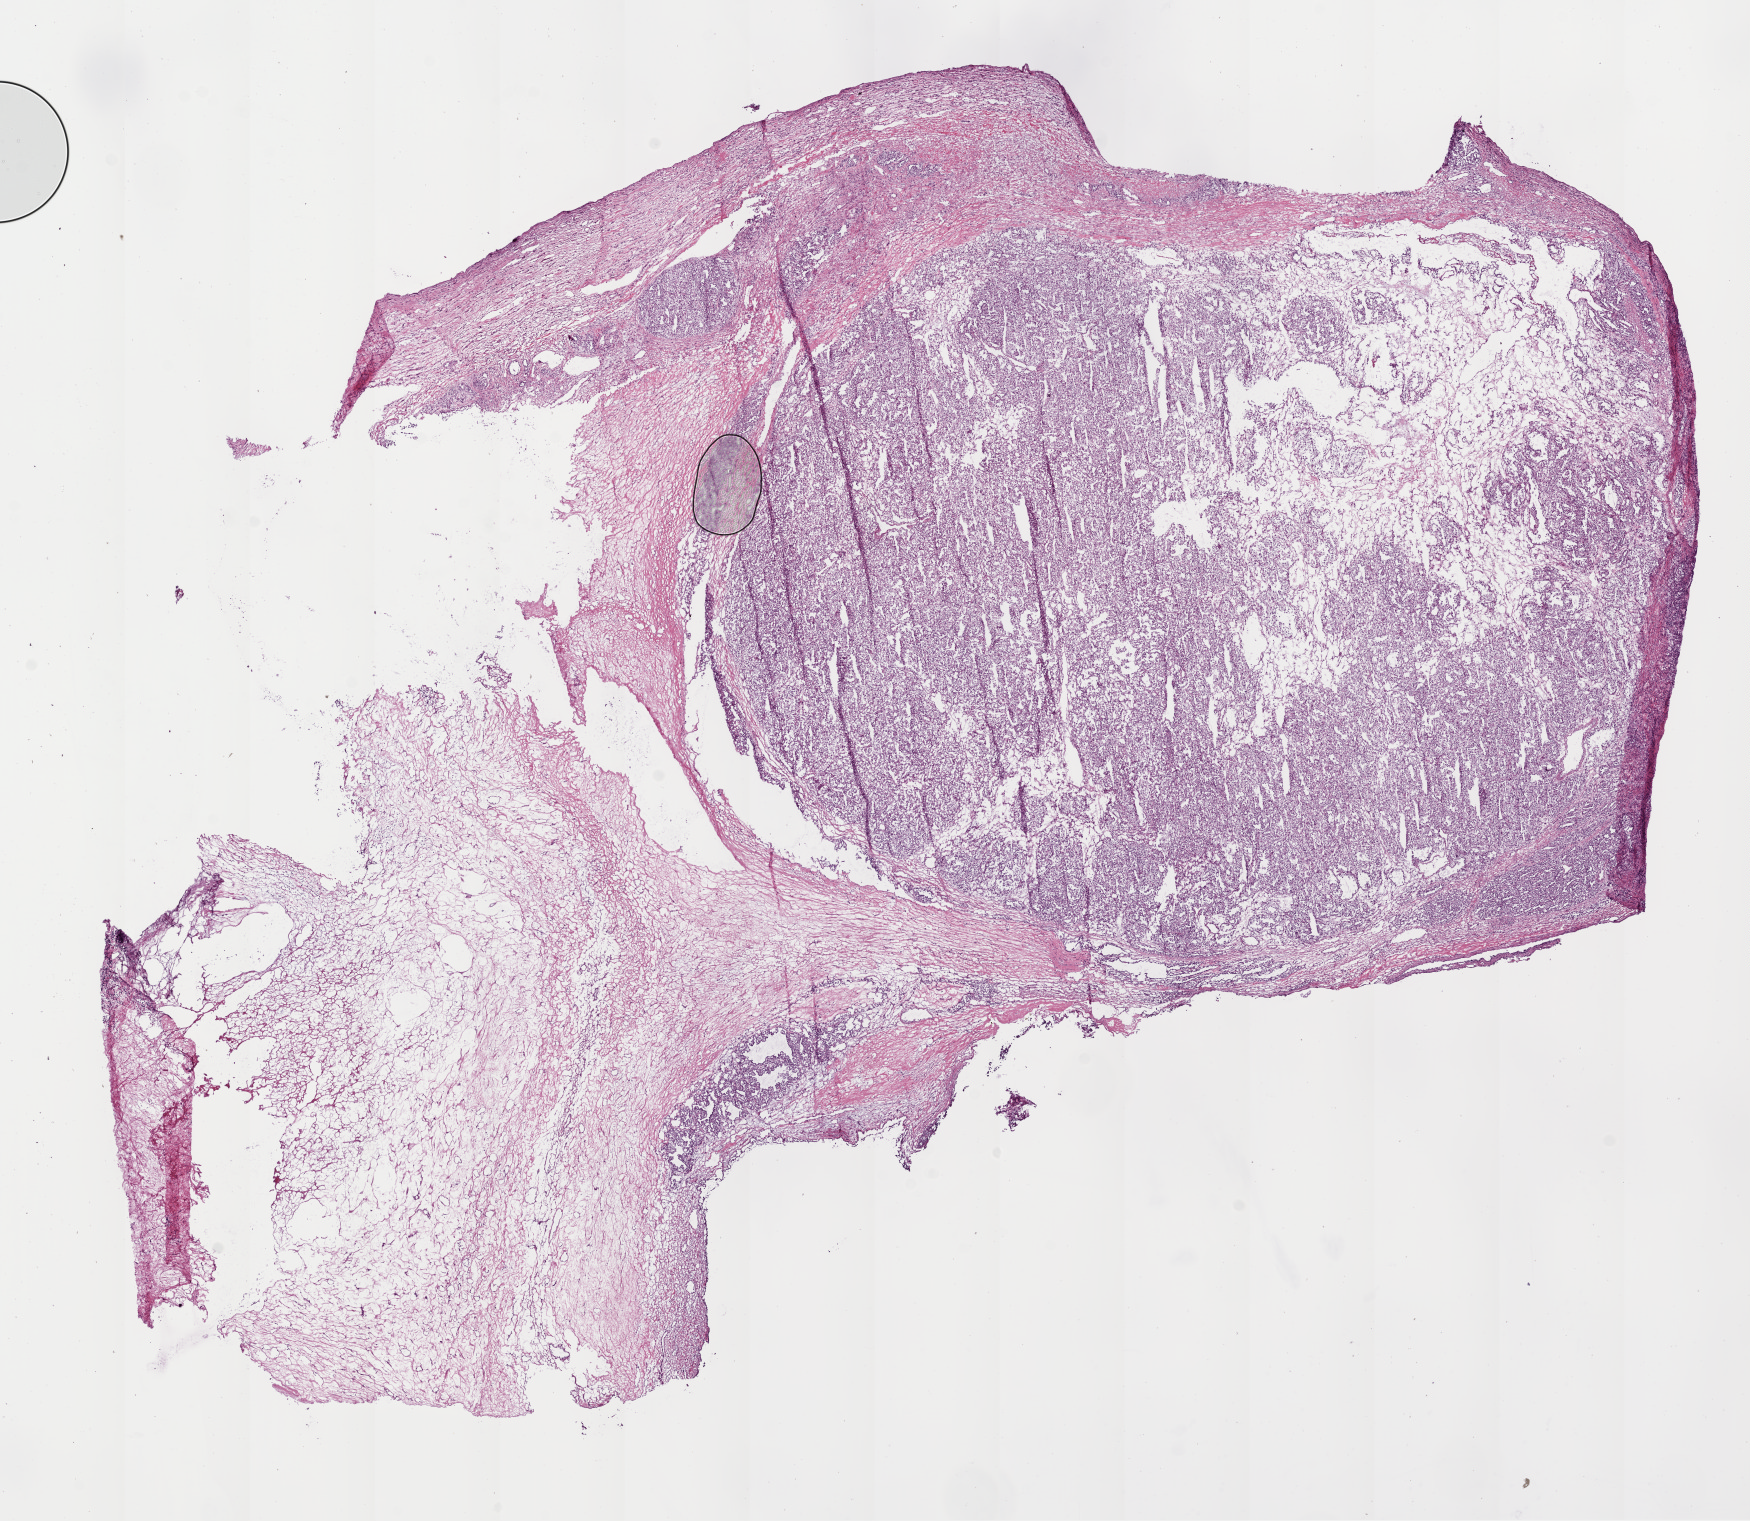
Hematoxylin and eosin (H&E) stained whole-slide image — low-resolution overview of the scanned area, about 14.0 x 12.2 mm (acquisition: 20x scan). Frozen section from the bottom of the tissue portion. Primary tumour sample from the kidney. Female, age 55 years at initial diagnosis. Histologic grade: G2 (moderately differentiated). Composition of this section per pathologist review: tumour cells 60%, tumour nuclei 80%, normal cells 0%, stromal cells 40%, necrosis 0%.
Histologic diagnosis: Clear cell adenocarcinoma, NOS. AJCC pathologic stage: I. TNM: T1a NX M0. Laterality: left.